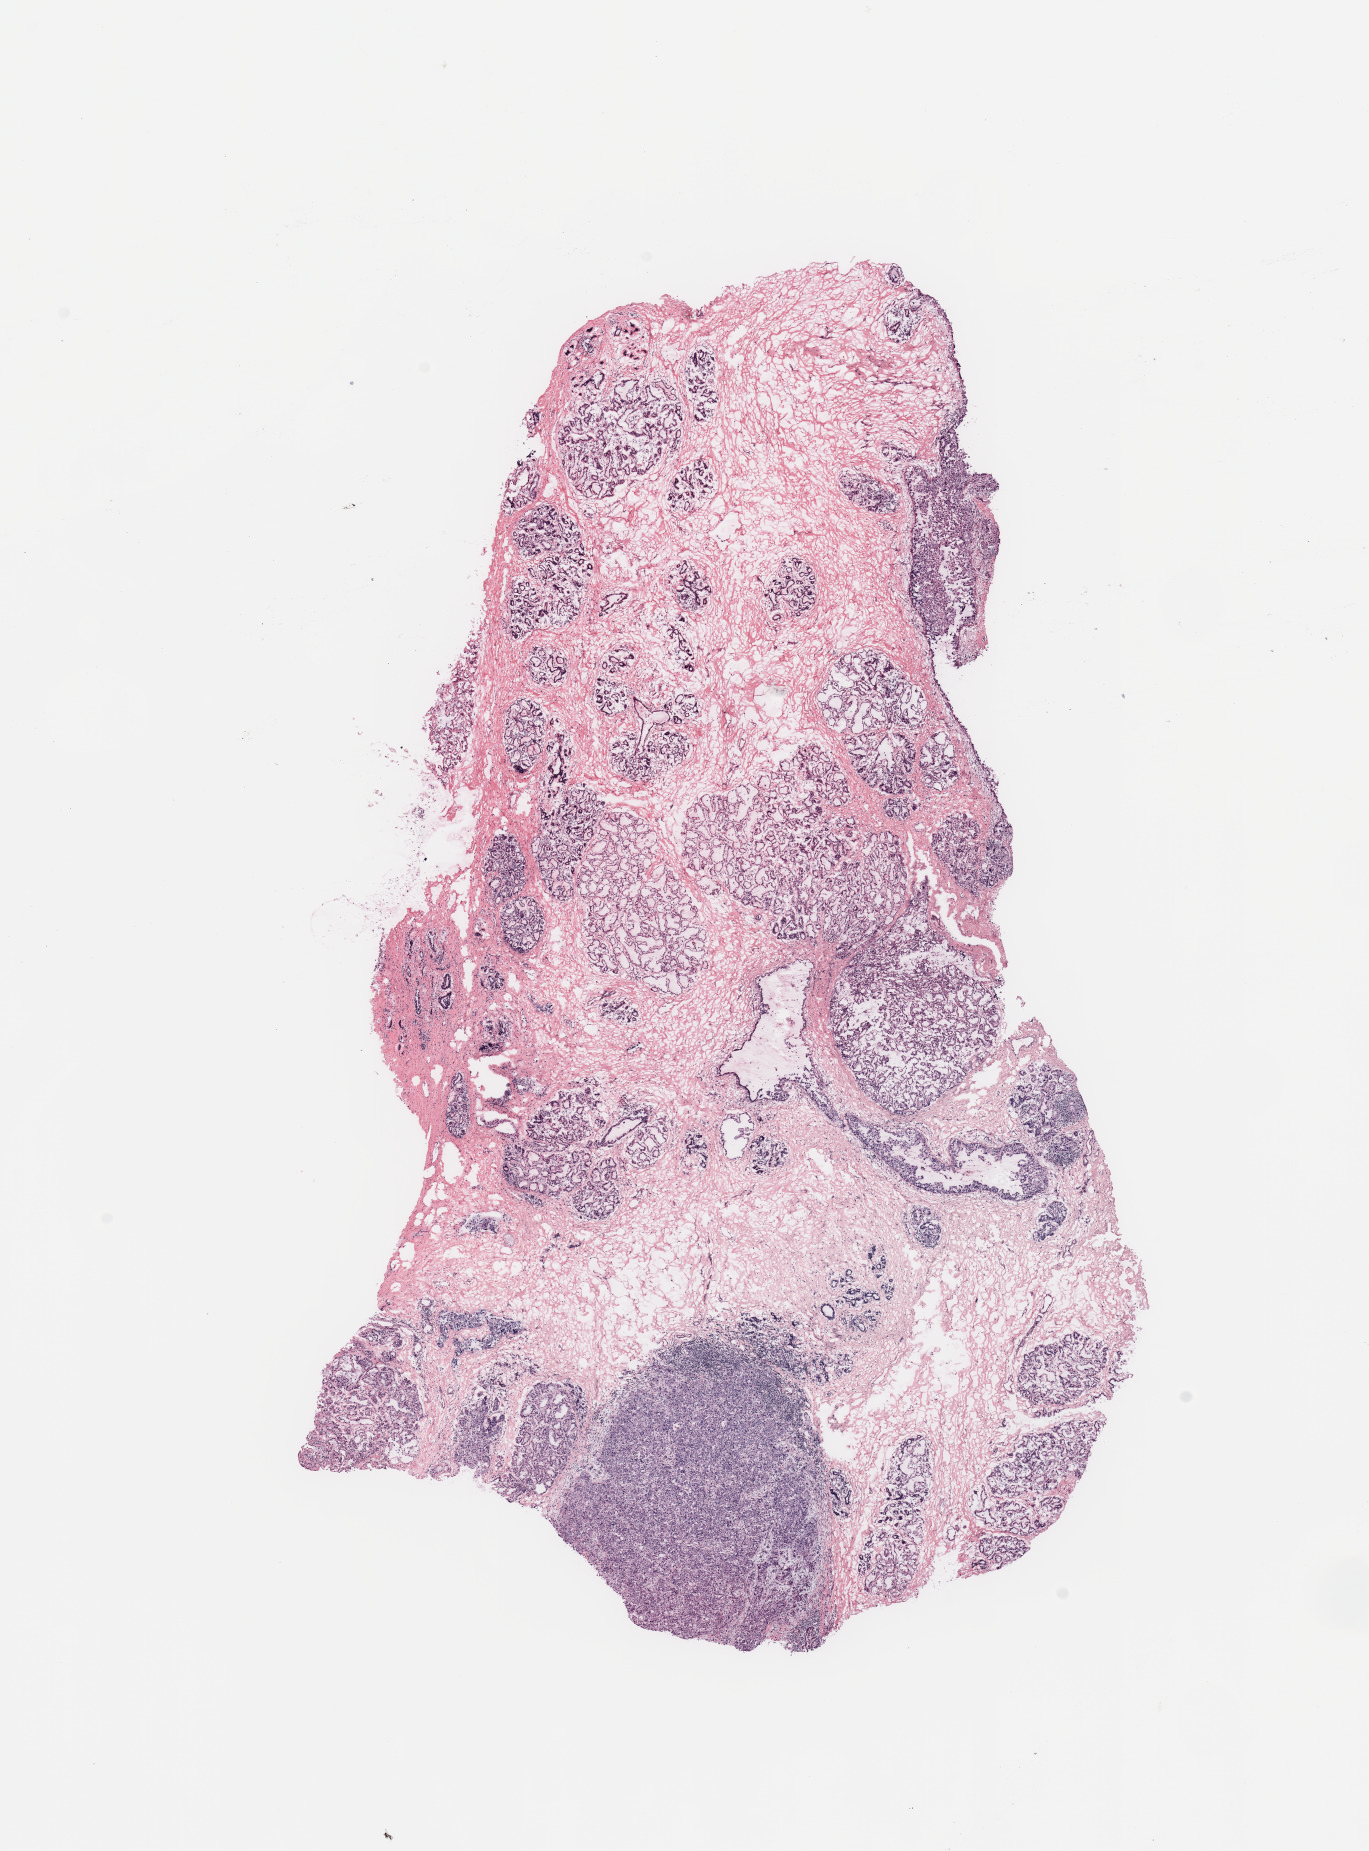
Whole-slide histology image, H&E-stained — a low-resolution overview of the entire scanned area, about 10.8 x 14.6 mm (slide scanned at 20x). Tumour tissue sample, breast. 40-year-old female patient.
- AJCC pathologic stage: IIB
- histologic diagnosis: Infiltrating duct carcinoma, NOS